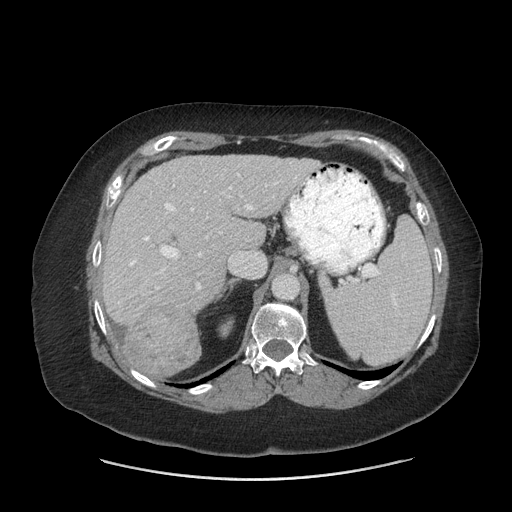
Contrast-enhanced abdominal CT (liver protocol), one axial slice; position 45 of 69 along the scan axis; reconstruction kernel STANDARD; soft-tissue window (W 400 / L 40 HU); 2.5 mm slice thickness; 512 × 512 image matrix. Case-level facts recorded for this patient, not image findings: diagnosis: hepatocellular carcinoma (patient treated with transarterial chemoembolisation; whether this scan precedes or follows treatment is not stated here); TNM stage (as recorded): Stage-IIIB; Child-Pugh class: A; tumour differentiation: moderately differentiated; tumour nodularity: multinodular.
Annotated regions visible in this slice (semi-automatically segmented with operator editing):
- liver parenchyma outside the tumour (the mass and vessels are separate outlines, so this box may not span the whole liver): box from (x=102, y=154) to (x=320, y=339) px
- mass: (x=125, y=303)–(x=201, y=378)
- liver vessels: (x=129, y=173)–(x=298, y=290)